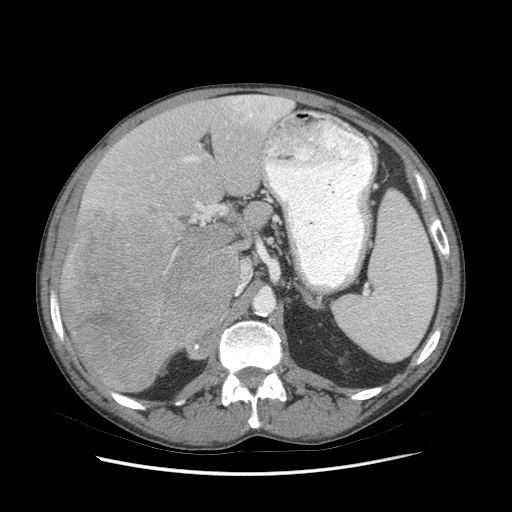
Contrast-enhanced abdominal CT (liver protocol), one axial slice. Slice 46 of 89 in the series (ordered by position). 140 kVp. Soft-tissue window (W 400 / L 40 HU). 2.5 mm slice thickness. 512 × 512 image matrix, field of view 380 × 380 mm. From the clinical record (not read from this slice): diagnosis: hepatocellular carcinoma (patient treated with transarterial chemoembolisation; whether this scan precedes or follows treatment is not stated here); TNM stage (as recorded): Stage-IIIB; Child-Pugh class: A; tumour differentiation: moderately differentiated; tumour nodularity: multinodular.
Structures marked on this image (semi-automatic segmentation, software-assisted and operator-edited):
- liver parenchyma outside the tumour (the mass and vessels are separate outlines, so this box may not span the whole liver): bounding box (x1, y1, x2, y2) in pixels: (60, 94, 292, 392)
- mass: (58, 206, 240, 390)
- liver vessels: (95, 96, 291, 225)